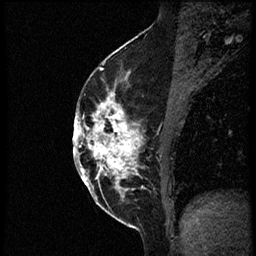
Breast MRI (dynamic contrast-enhanced), one sagittal slice; position 31 of 56 along the scan axis; dynamic contrast-enhanced study with each time point stored as its own series, time point 2 of 3 at this slice position (early post-contrast, ordered by acquisition time); 1.5 T; TE 4.2 ms, TR 21.3 ms; 2 mm slice thickness; 256 × 256 image matrix. Patient: female, 41 years. Case-level facts recorded for this patient, not image findings: setting: breast cancer imaged before/during neoadjuvant chemotherapy; receptor status: HER2-positive.
Annotated regions visible in this slice (semi-automatically segmented with operator editing):
- analysis volume of interest (the breast-tissue region the enhancement analysis was run in; not a lesion): bounding box [x1, y1, x2, y2] px = [86, 73, 177, 205]
- tumour enhancement mask (voxels above the 100 % enhancement threshold inside the analysis volume of interest): [86, 73, 144, 196]